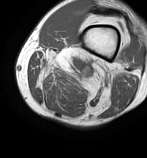
MRI of an extremity soft-tissue mass, one axial slice; position 19 of 86 along the scan axis; MR volume resampled by the dataset authors to the PET/CT grid (not the native acquisition matrix); 147 × 158 image matrix. Male patient. From the clinical record (not read from this slice): histological type: undifferentiated pleomorphic liposarcoma; grade: high; site of the primary tumour: left thigh.
Annotated regions visible in this slice (expert contour drawn on MRI and transferred to this co-registered scan by the dataset authors):
- gross tumour volume including surrounding oedema: box from (x=37, y=47) to (x=120, y=93) px